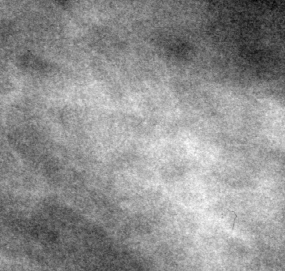
Region of interest cut from a scanned film mammogram (one marked finding), left breast, MLO view, BI-RADS breast density category 3 (scale 1–4).
Finding: mass, shape irregular, margins ill defined; BI-RADS assessment category 3; pathology (as recorded): benign.